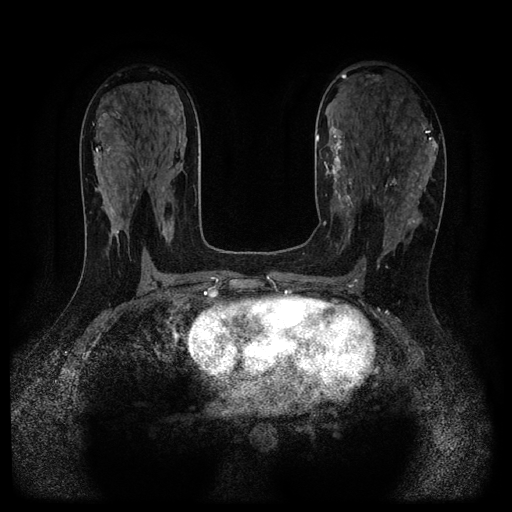
Breast MRI (dynamic contrast-enhanced, multi-phase), one axial slice; slice 59 of 116 in the series (ordered by position); dynamic contrast-enhanced series, time point 2 of 5 at this slice position (early post-contrast); 1.5 T; TE 2.7 ms, TR 5.4 ms; 2.2 mm slice thickness; 512 × 512 image matrix, field of view 330 × 330 mm. Patient: female, 43 years.
Outlined on this slice (semi-automatic segmentation, software-assisted and operator-edited):
- breast lesion (labelled benign in the annotation): box from (x=324, y=120) to (x=358, y=228) px